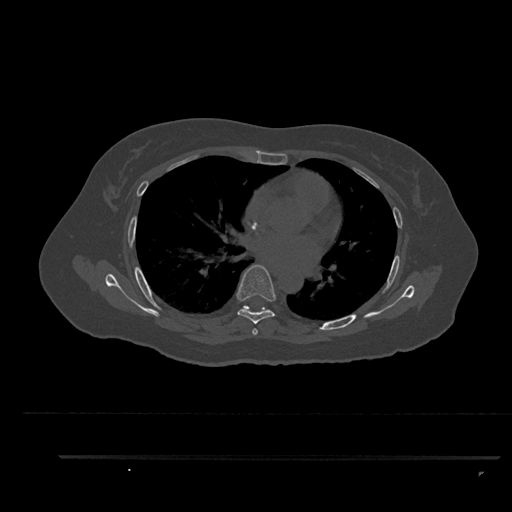
CT including the spine, one axial slice. Slice 553 of 797 in the series (ordered by position). Reconstruction kernel Br40s/3. Bone window (W 1800 / L 400 HU). 512 × 512 image matrix, field of view 408 × 408 mm. Patient: female, 44 years. From the clinical record (not read from this slice): primary cancer: renal; vertebrae with lytic lesions (as recorded): L1.
Structures marked on this image (semi-automatically segmented with operator editing):
- T6 vertebra: bounding box [x1, y1, x2, y2] px = [236, 264, 276, 335]